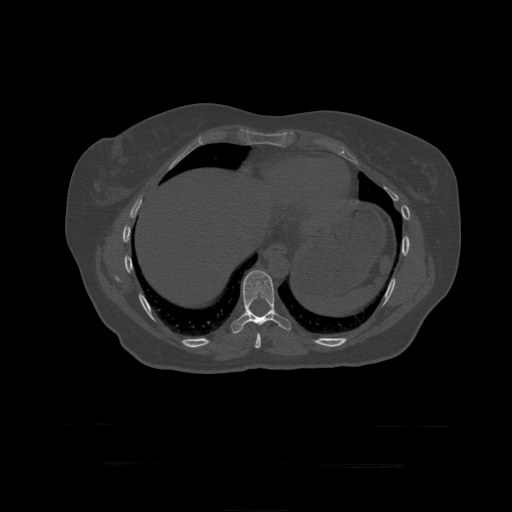
CT including the spine, one axial slice. Position 244 of 399 along the scan axis. 120 kVp. Bone window (W 1800 / L 400 HU). 1.25 mm slice thickness. 512 × 512 image matrix, field of view 450 × 450 mm. Patient age 41 years. Case-level facts recorded for this patient, not image findings: primary cancer: breast.
Structures marked on this image (semi-automatically segmented with operator editing):
- T10 vertebra: box from (x=231, y=270) to (x=291, y=334) px
- T9 vertebra: (x=255, y=333)–(x=261, y=349)